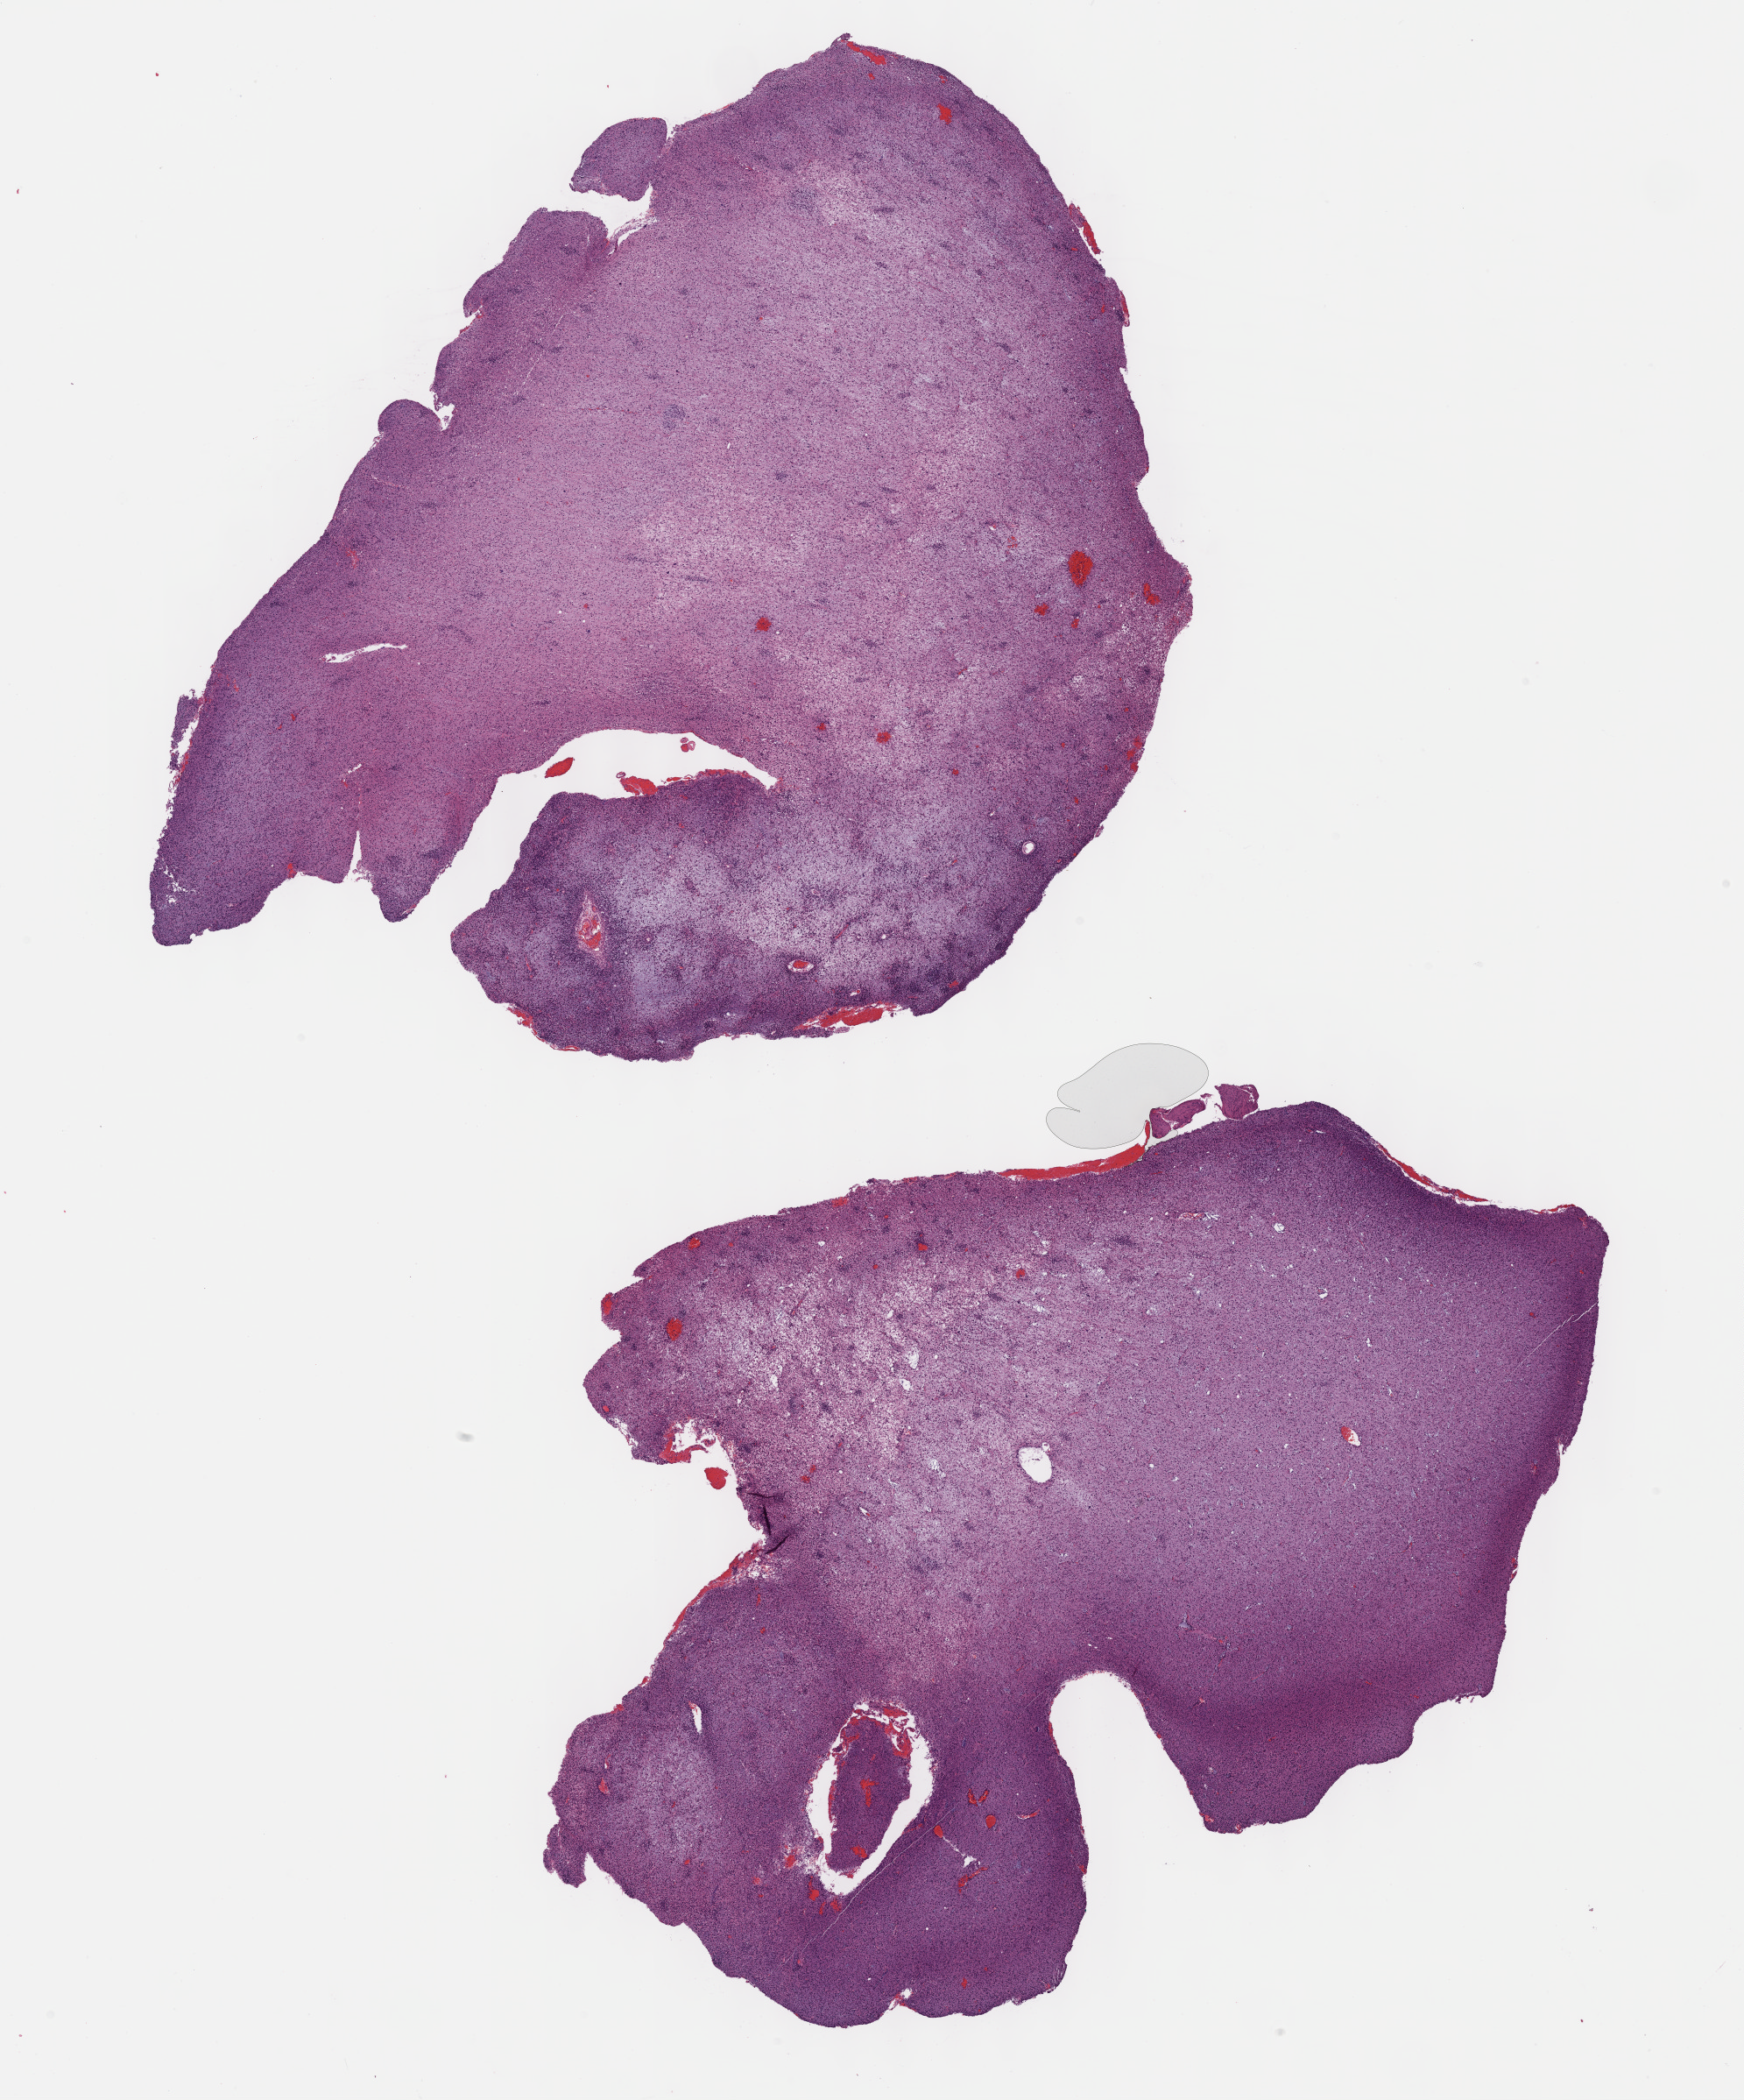
H&E whole-slide image — whole scanned area (about 16.1 x 19.4 mm) shown as a low-resolution overview; formalin-fixed paraffin-embedded (FFPE) diagnostic section; sample: primary tumour, brain. Male patient; age at initial diagnosis 67 years. Histologic grade: G3 (poorly differentiated).
Diagnosis: Mixed glioma.